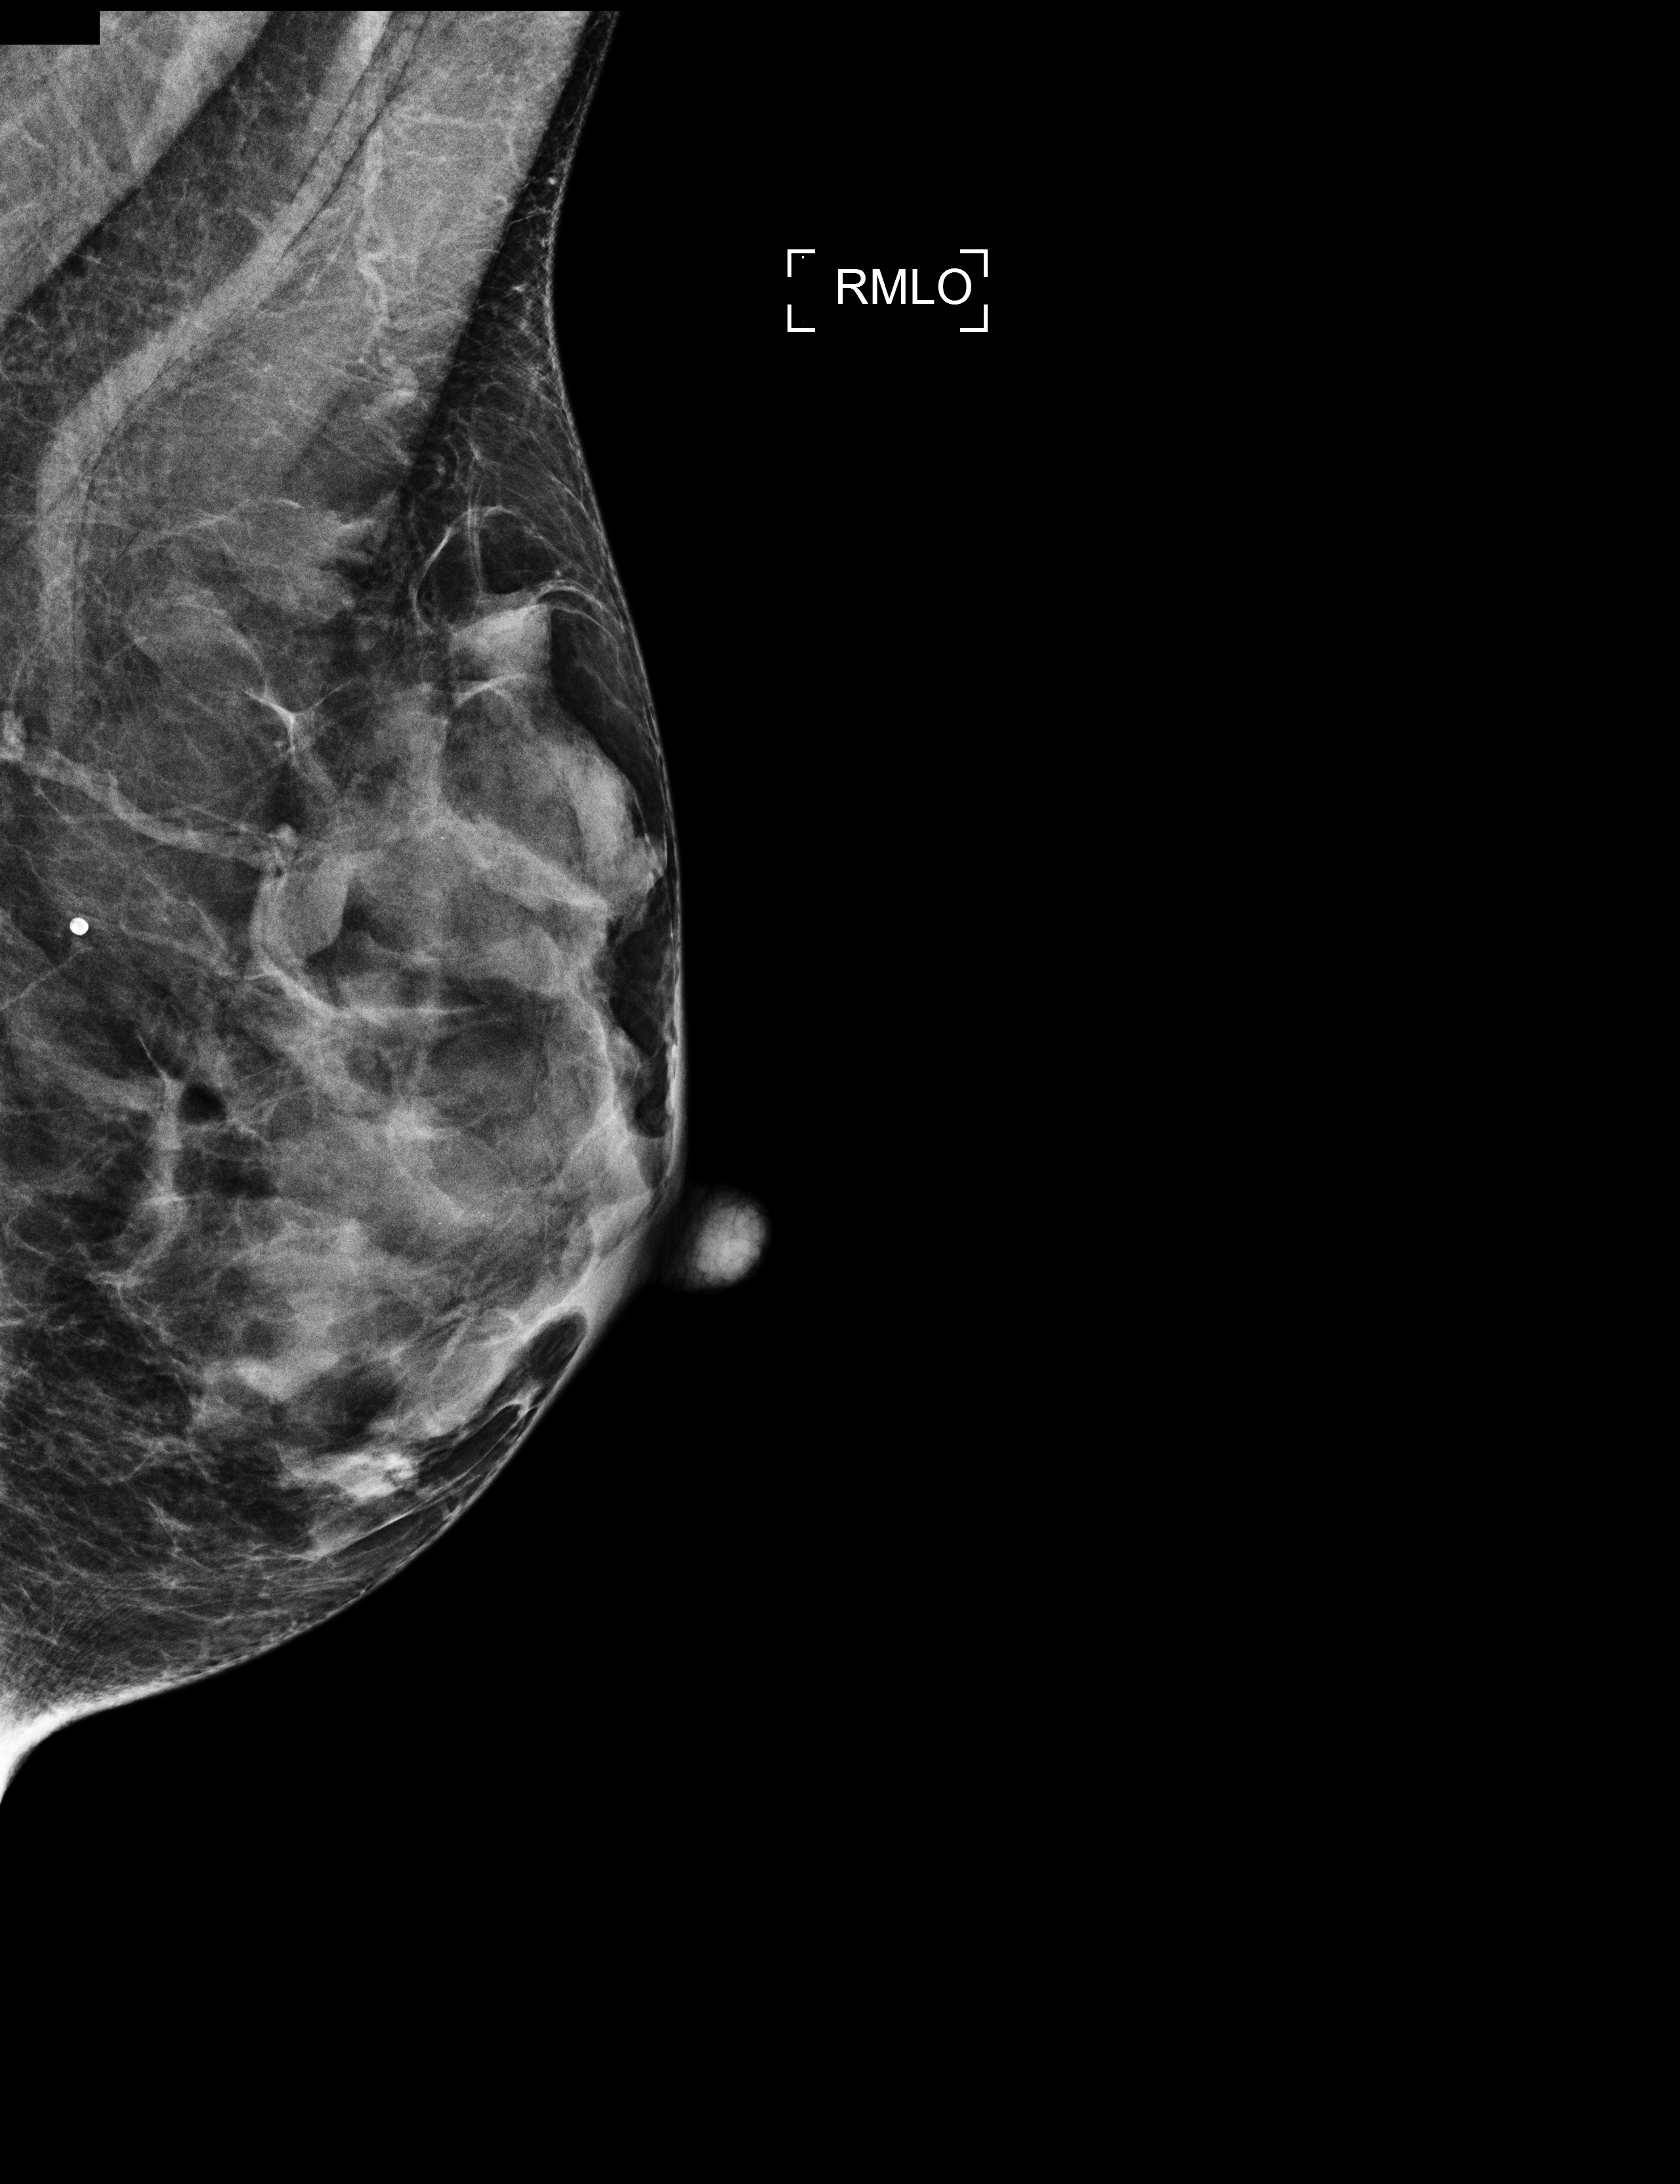
Annual screening mammography examination, compressed breast thickness 21 mm, system: Selenia Dimensions. Patient: female, 54 years.
Image type: full-field digital mammogram. Breast: right. Projection: MLO view.